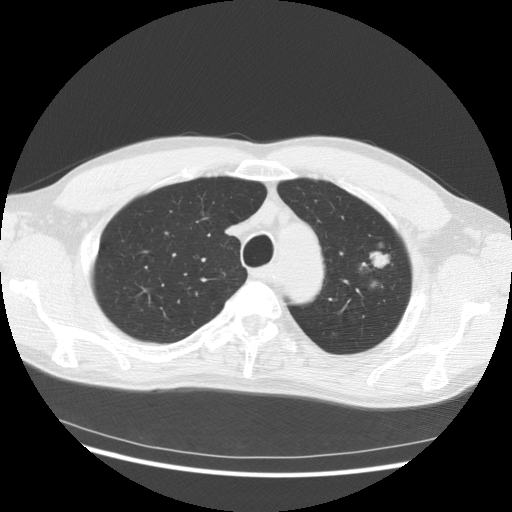
Low-dose screening chest CT, one axial slice; position 112 of 145 along the scan axis; reconstruction kernel STANDARD; lung window (W 1500 / L -600 HU); 2.5 mm slice thickness; 512 × 512 image matrix, field of view 370 × 370 mm.
Outlined on this slice (expert manual segmentation):
- lesion 1 (tumor, upper lobe of left lung): bounding box <370,252,389,267> (left, top, right, bottom; pixels)